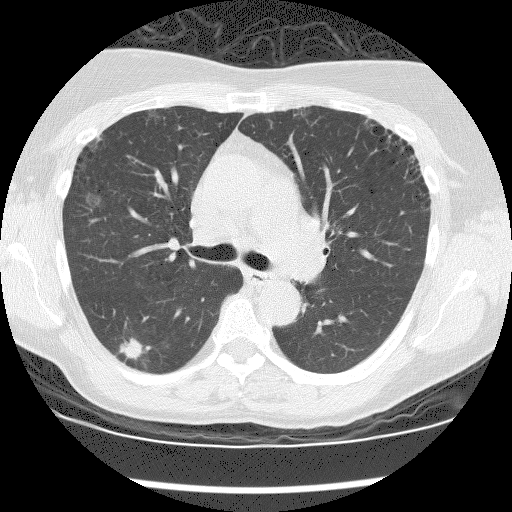
Low-dose screening chest CT, one axial slice. Slice 118 of 176 in the series (ordered by position). Reconstruction kernel BONE. Lung window (W 1500 / L -600 HU). 512 × 512 image matrix.
Outlined on this slice (expert manual segmentation):
- lesion 1 (tumor, lower lobe of right lung): bounding box <120,338,151,360> (left, top, right, bottom; pixels)